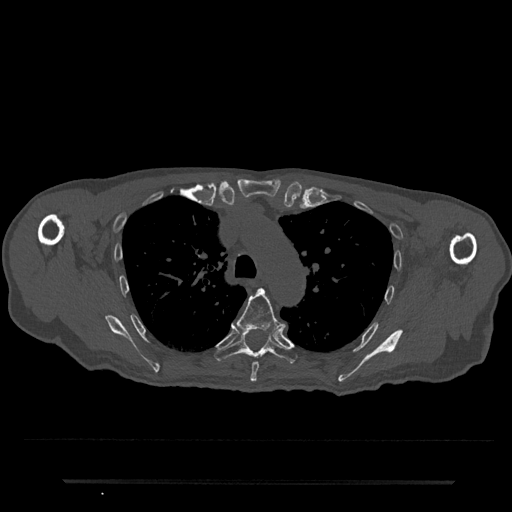
CT including the spine, one axial slice. Slice 556 of 797 in the series (ordered by position). Bone window (W 1800 / L 400 HU). 0.5 mm slice thickness. 512 × 512 image matrix, field of view 427 × 427 mm. Male patient, age 74 years. From the clinical record (not read from this slice): primary cancer: prostate.
Structures marked on this image (semi-automatic segmentation, software-assisted and operator-edited):
- T5 vertebra: box from (x=237, y=288) to (x=286, y=382) px
- T6 vertebra: (x=214, y=332)–(x=298, y=363)